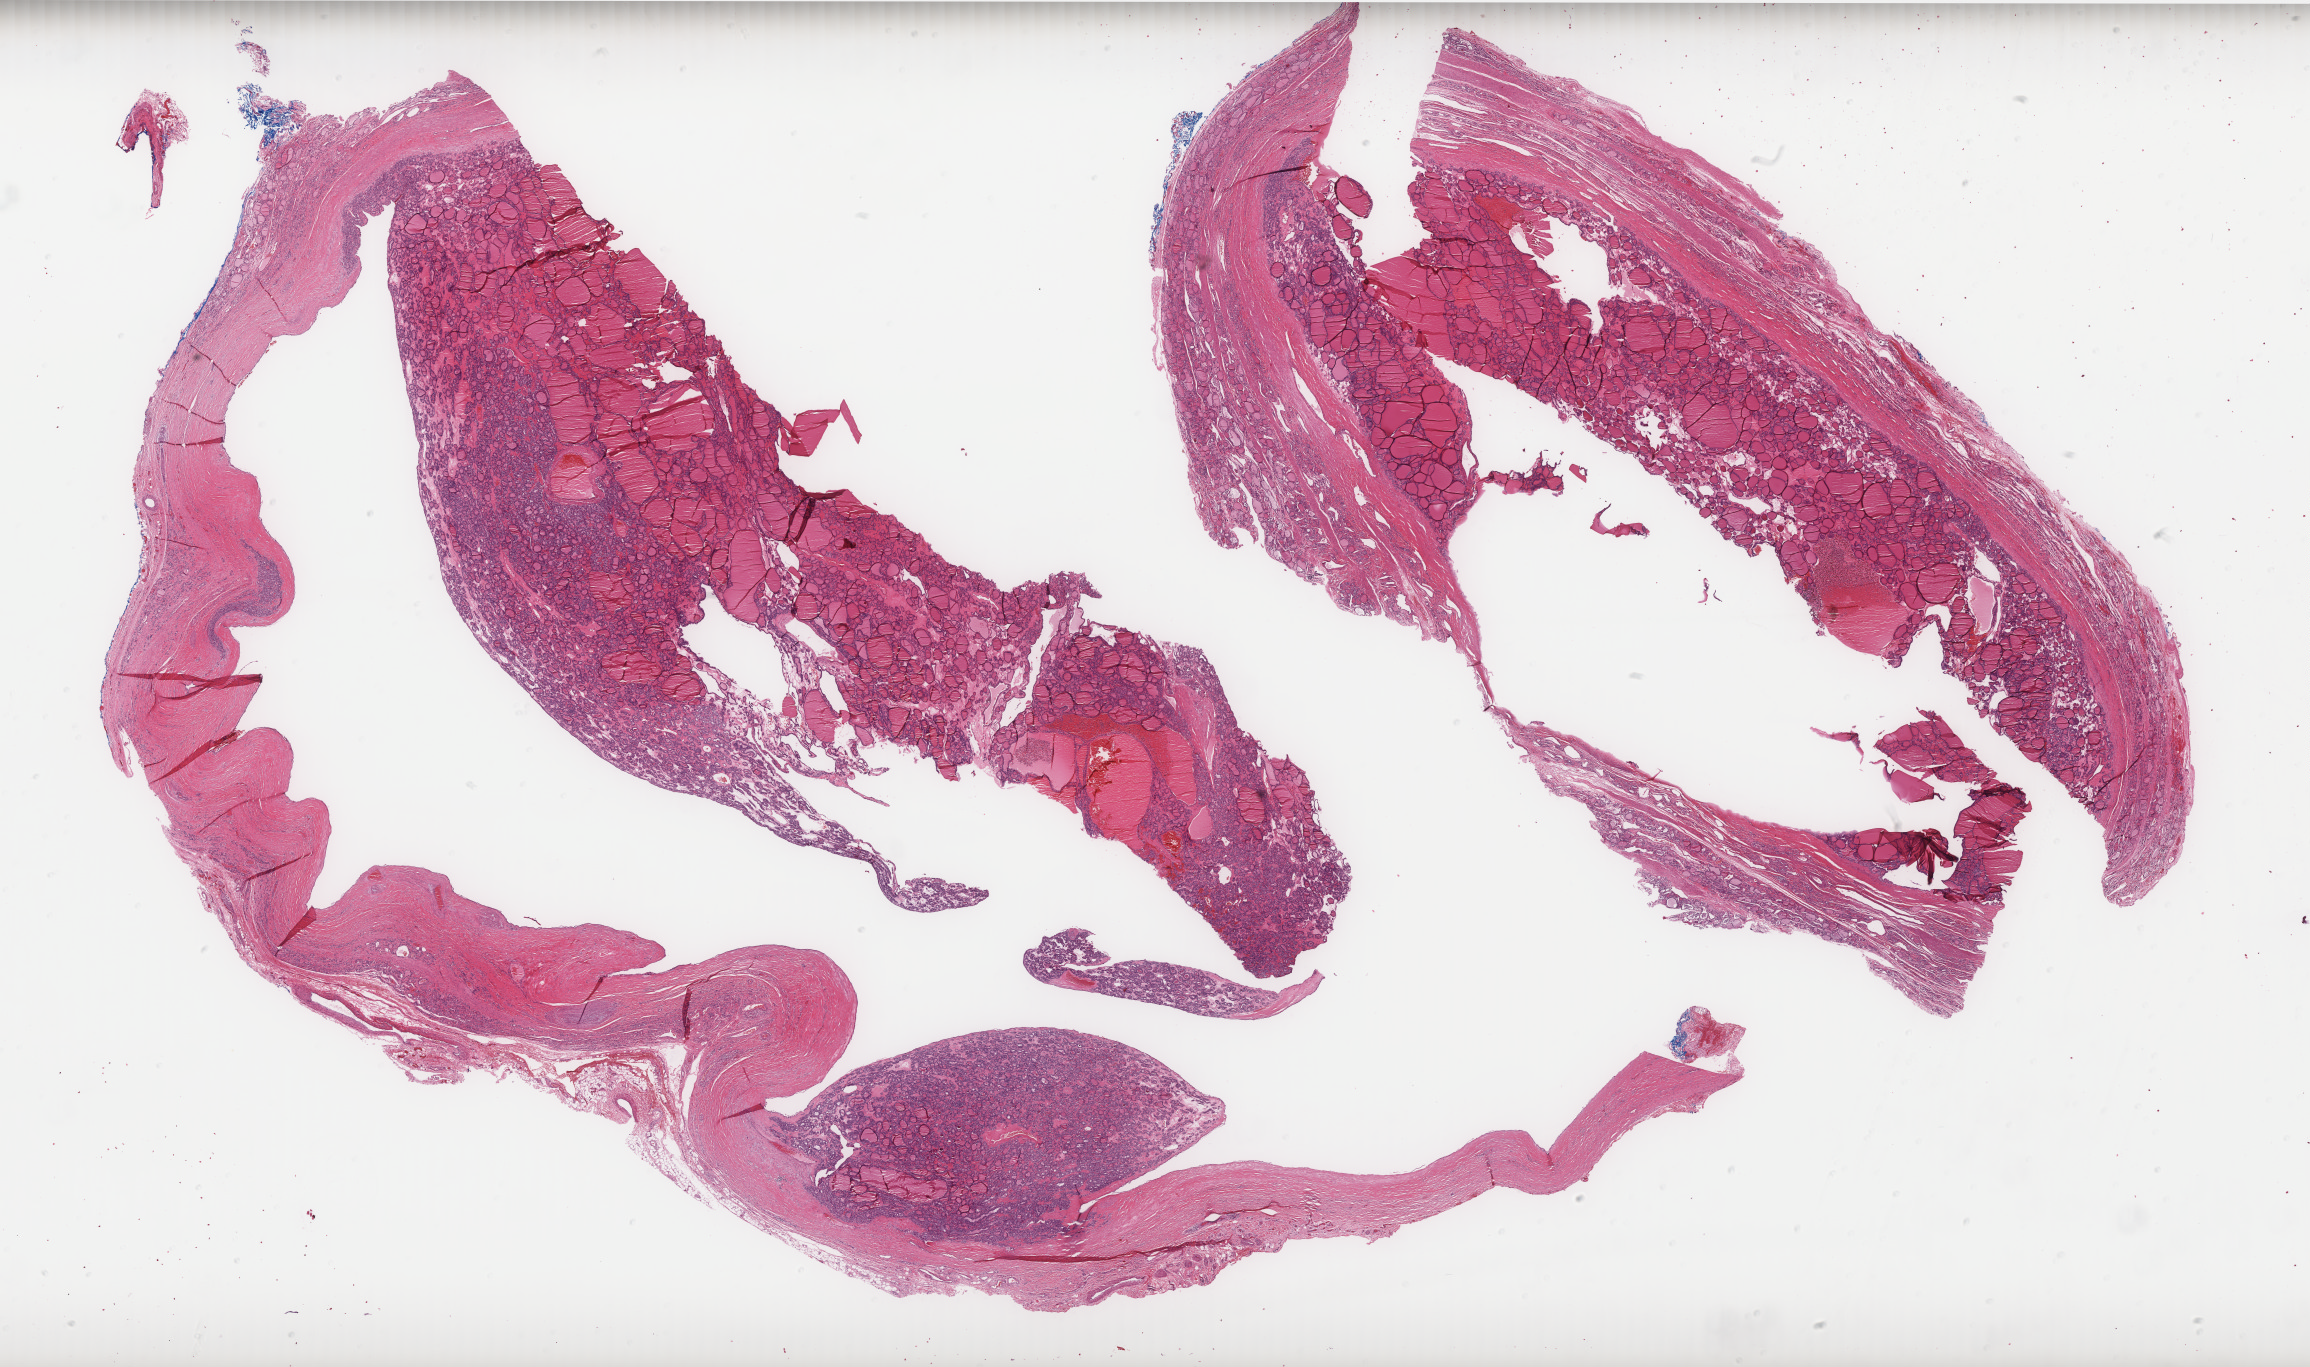
Digitized Hematoxylin and eosin (H&E) stained tissue section (whole slide) — a low-resolution overview of the entire scanned area, about 37.0 x 21.9 mm (slide scanned at 40x). Formalin-fixed paraffin-embedded (FFPE) diagnostic section. Primary tumour sample from the thyroid. Male patient; age at initial diagnosis 55 years.
• lymph nodes positive (case pathology): 0 of 5 examined
• AJCC pathologic stage: II
• histologic diagnosis: Papillary adenocarcinoma, NOS (thyroid gland)
• TNM: T2 N0 MX
• laterality: right